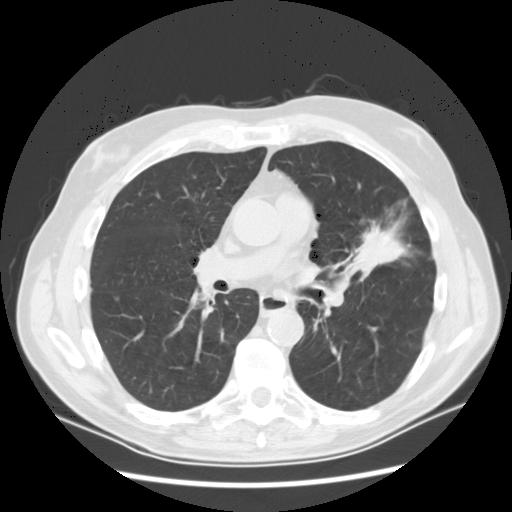
Axial slice from a low-dose chest CT screening exam. Baseline screening round. Lung window (W 1500 / L -600 HU). 512 × 512 image matrix, field of view 380 × 380 mm. Male, age 65 years at enrolment. Current smoker at enrolment.
Expert reader's lesion annotation, bounding box <348,208,415,277> (left, top, right, bottom; pixels). Reader record for this screening exam (exam-level; its link to the box is not recorded): non-calcified nodule or mass ≥4 mm, left upper lobe, 37 × 27 mm, spiculated (stellate) margins, soft tissue attenuation.